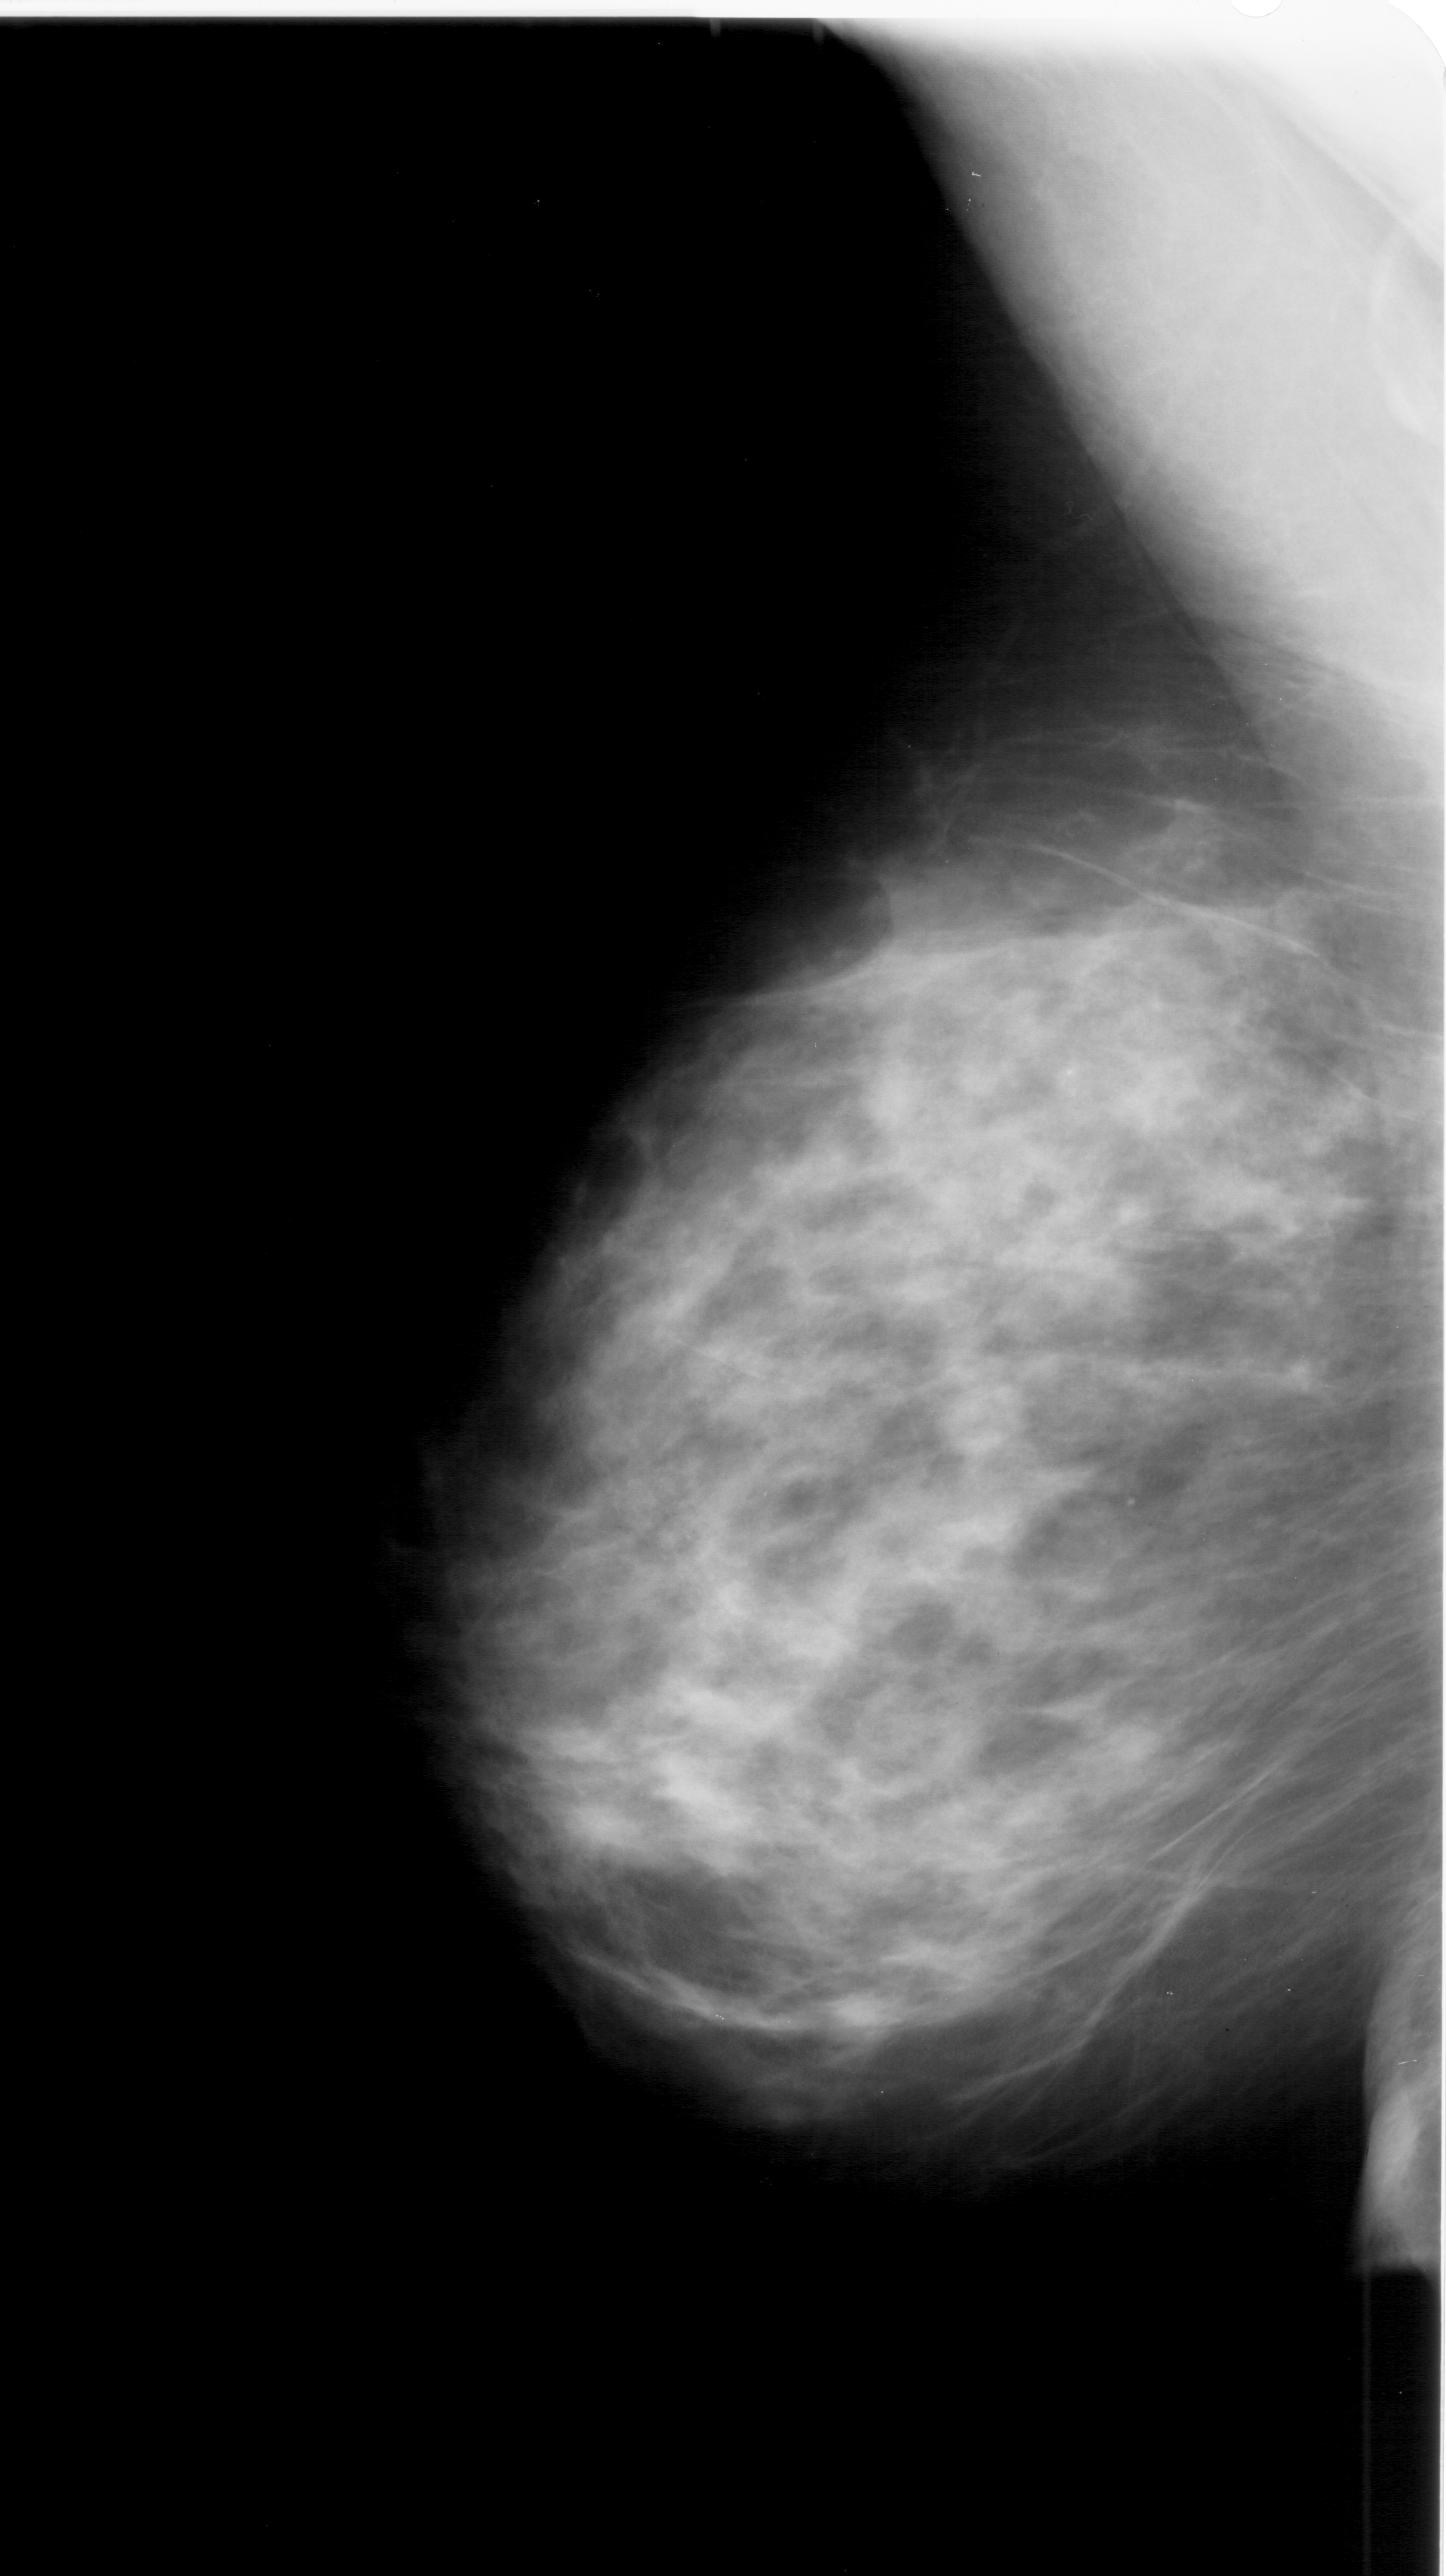
Digitized screen-film mammogram, left breast, mediolateral oblique (MLO) view, BI-RADS breast density category 4 (scale 1–4).
Abnormality record for this image: calcifications, morphology pleomorphic, distribution clustered; BI-RADS assessment category 4; pathology result (as recorded, not read from the image): benign.